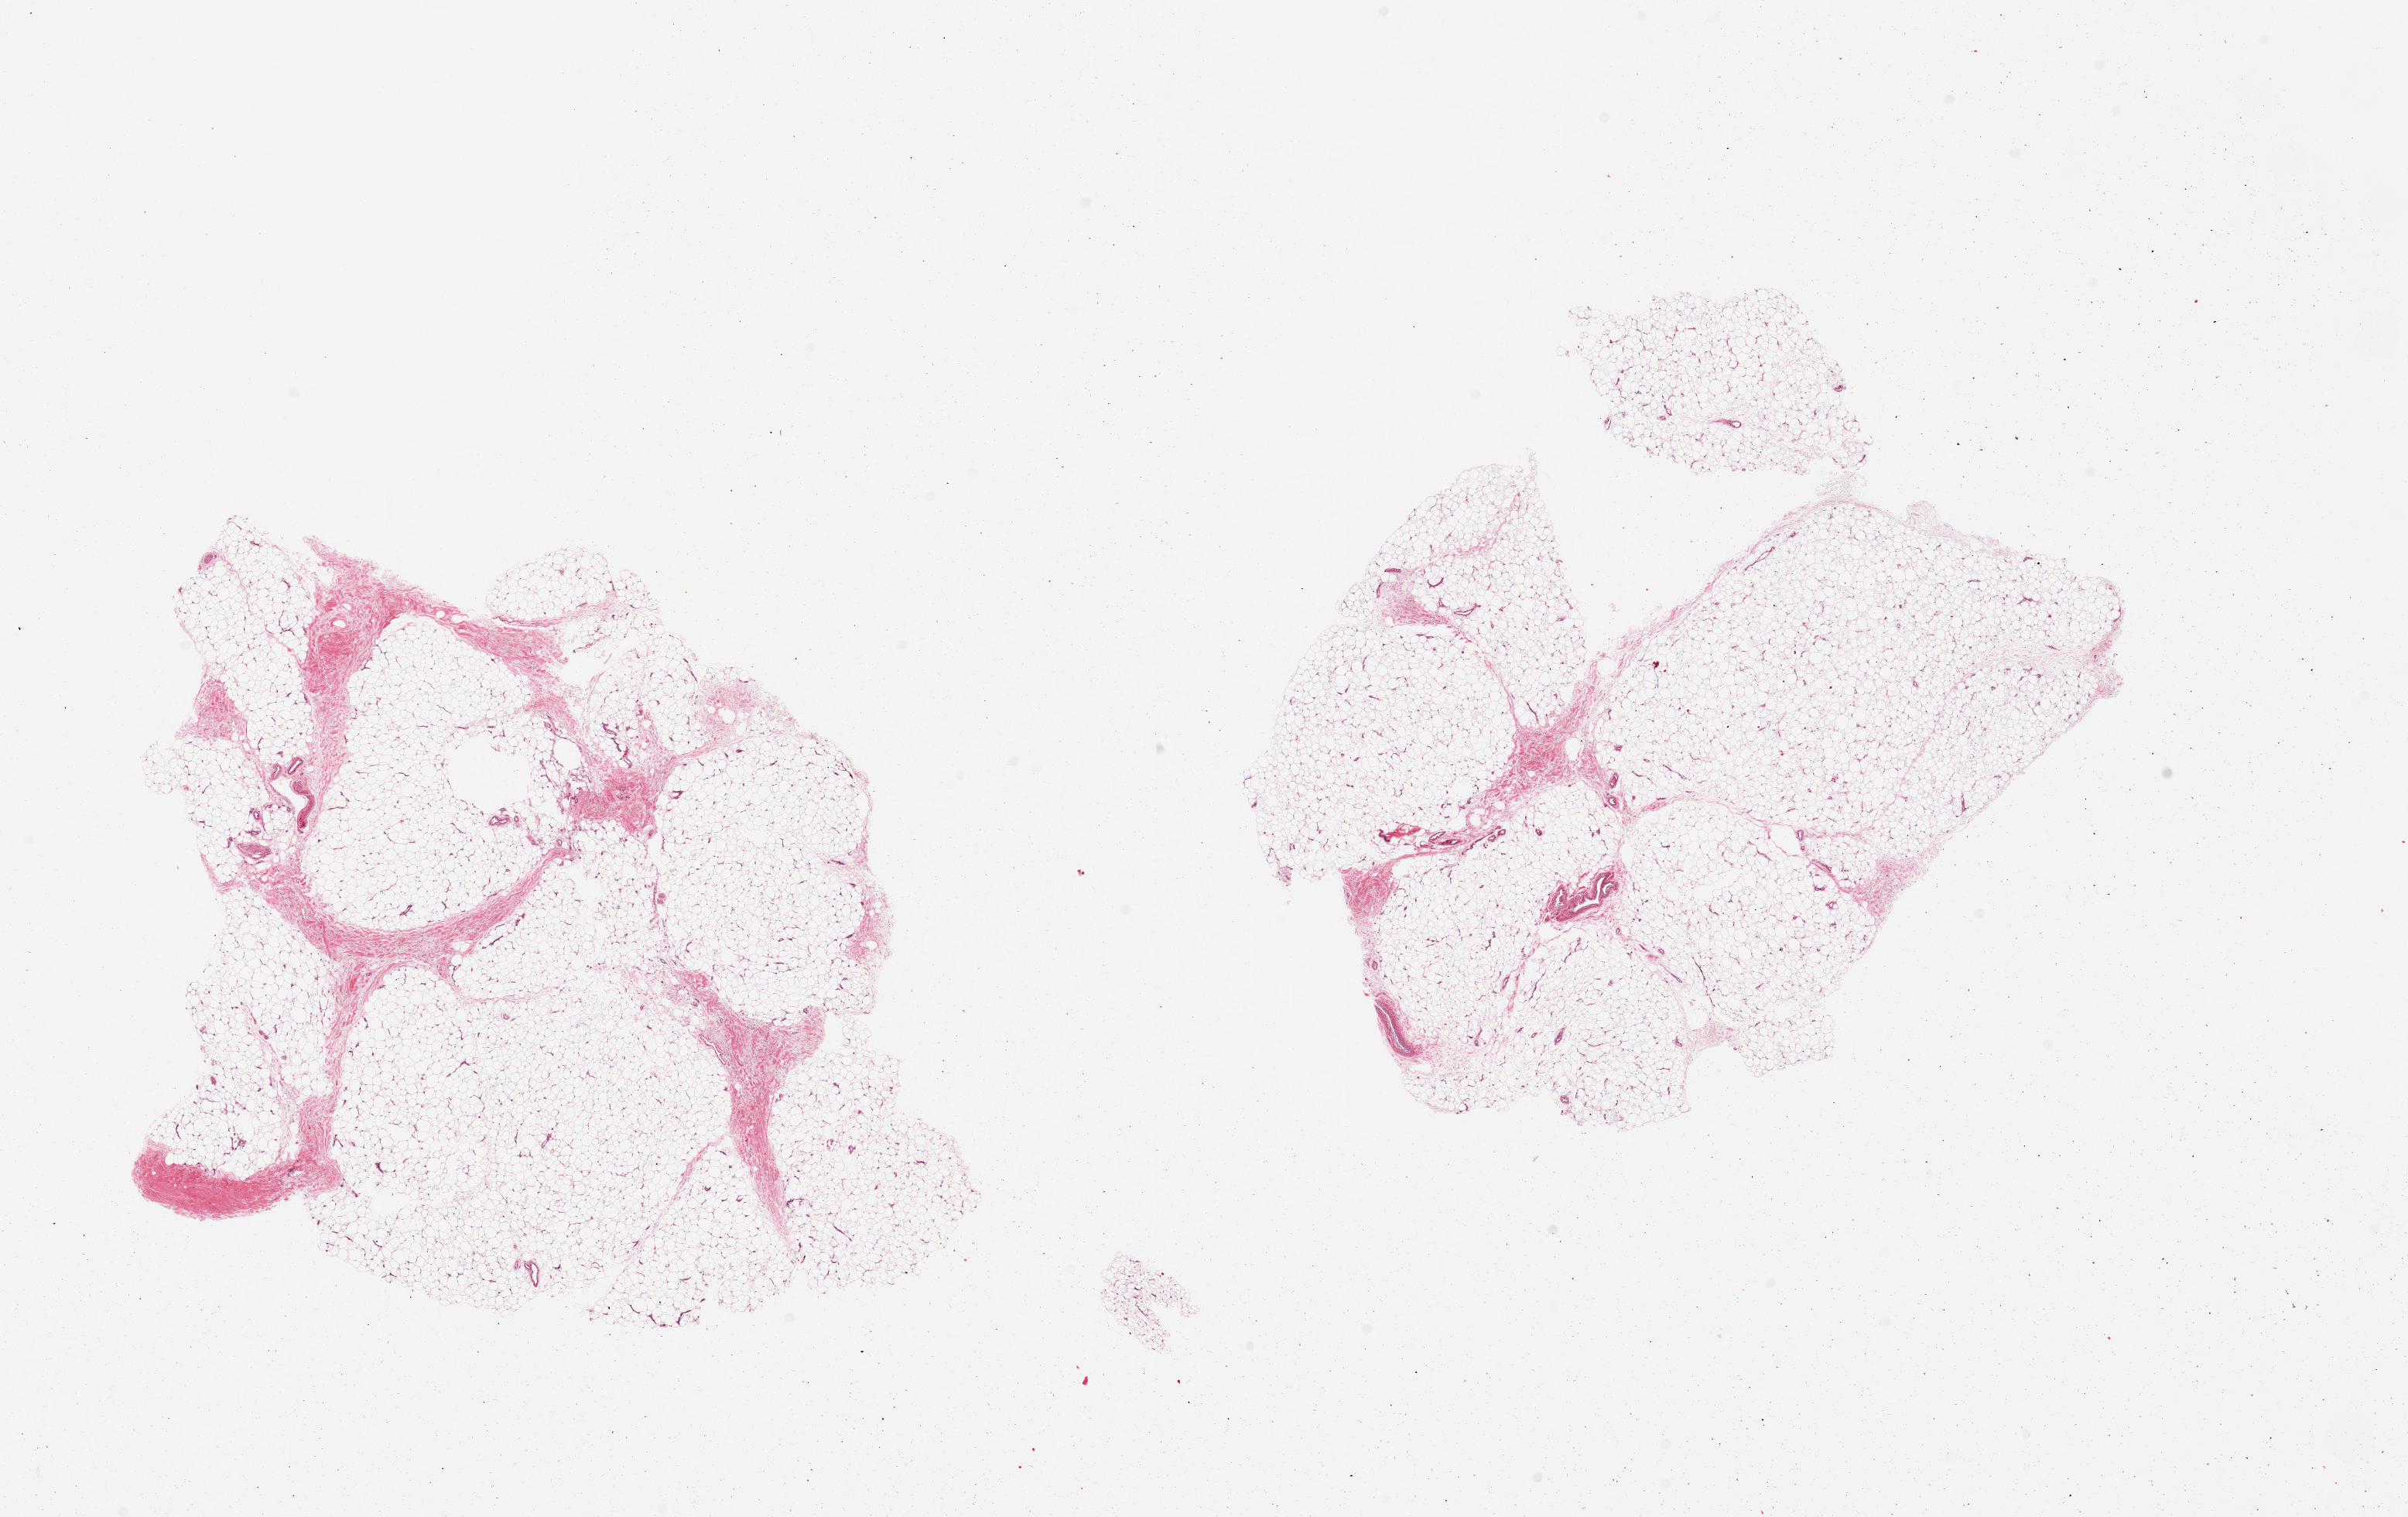
Digitized haematoxylin and eosin-stained section, brightfield, a low-resolution overview of the entire scanned area, about 24.6 x 15.5 mm (acquisition: 20x scan). PAXgene-fixed paraffin-embedded (PFPE) section. Target tissue: adipose tissue. Donor tissue sample. Male donor.
Pathologist's review note for this sample: 2 pieces; up to 5% fibrous content.